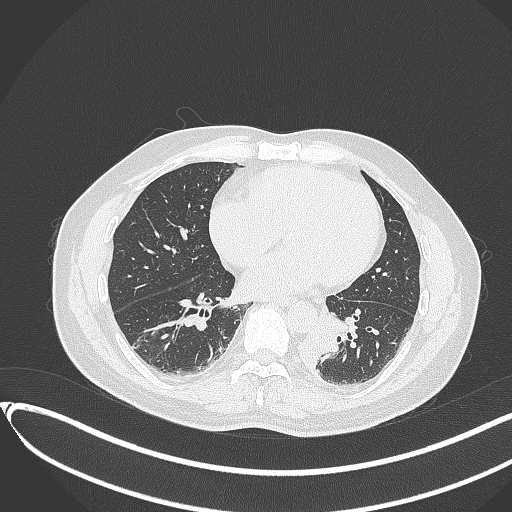
Chest CT, one axial slice. Reconstruction kernel B70f. 120 kVp. Lung window (W 1500 / L -600 HU). 512 × 512 image matrix, field of view 400 × 400 mm. Patient: male, 54 years. From the clinical record (not read from this slice): clinical TNM (as recorded): T3 N0 M0.
Annotated regions visible in this slice (rectangle marked by the reading radiologist):
- lung tumour (recorded histology: squamous cell carcinoma): bounding box <291,322,339,374> (left, top, right, bottom; pixels)